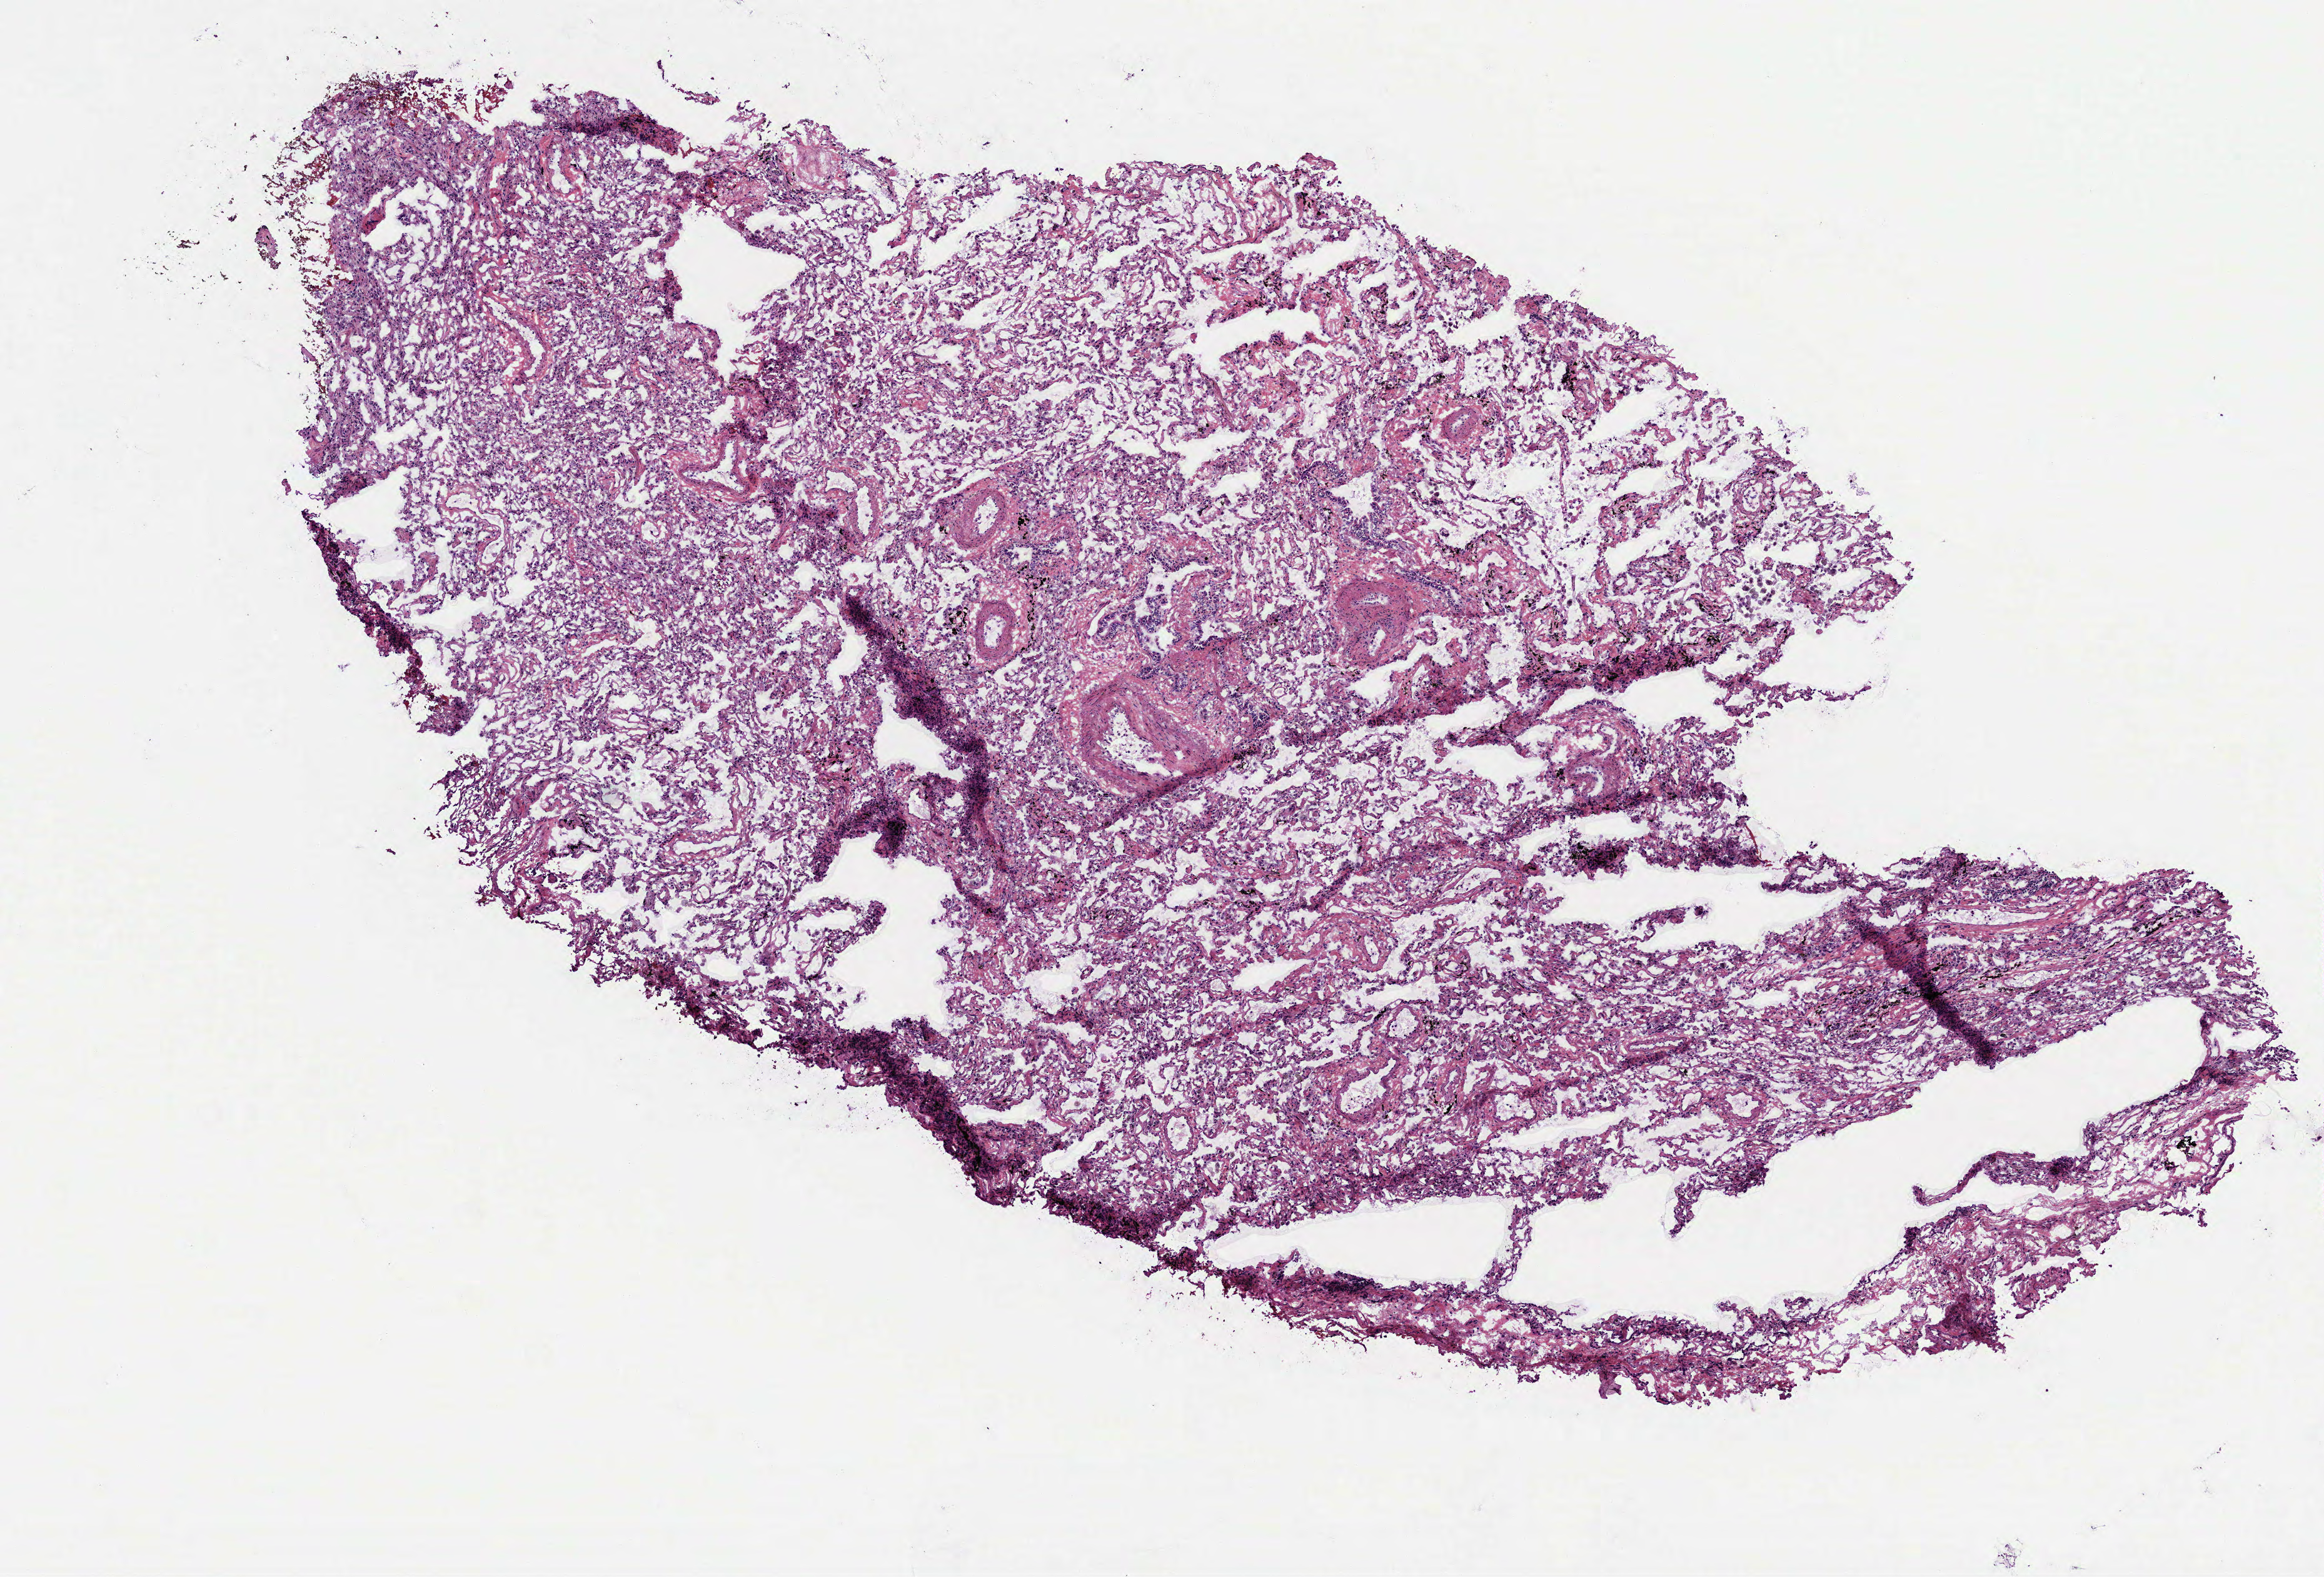
Whole-slide histology image, H&E-stained — low-resolution overview of the scanned area, about 7.5 x 5.1 mm (slide scanned at 40x), frozen section from the top of the tissue portion, sample: solid tissue normal (non-tumour tissue), lung. Patient: male, age at initial diagnosis 64 years. Inflammatory infiltration, as recorded: lymphocyte infiltration 2%, monocyte infiltration 15%, neutrophil infiltration 0%.
This section: solid tissue normal (non-tumour) sample from the same patient. Patient diagnosis: Squamous cell carcinoma, NOS (upper lobe, lung).